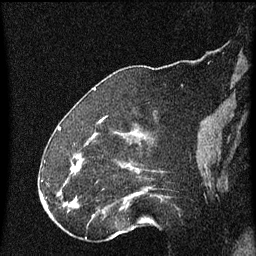
Breast MRI (dynamic contrast-enhanced), one sagittal slice; slice 22 of 60 in the series (ordered by position); dynamic contrast-enhanced series, image 2 of 4 at this slice position (ordered by acquisition); 1.5 T; TE 4.2 ms, TR 8 ms; 256 × 256 image matrix, field of view 180 × 180 mm. Patient: female, 52 years.
Structures marked on this image (semi-automatic segmentation, software-assisted and operator-edited):
- analysis volume of interest (the breast-tissue region the enhancement analysis was run in; not a lesion): bounding box (x1, y1, x2, y2) in pixels: (73, 152, 159, 219)
- tumour enhancement mask (voxels above the 70 % enhancement threshold inside the analysis volume of interest): (73, 166, 130, 207)